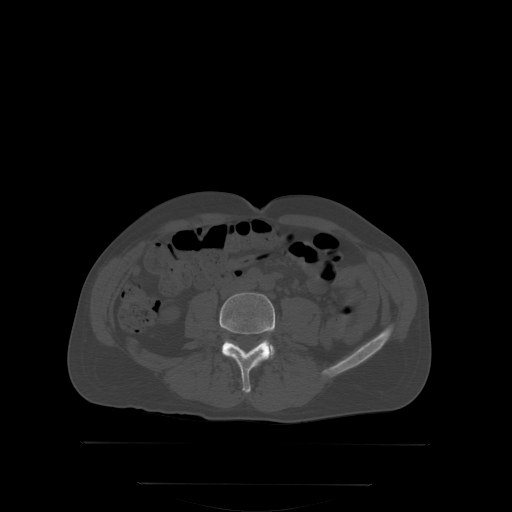
CT including the spine, one axial slice; slice 106 of 350 in the series (ordered by position); bone window (W 1800 / L 400 HU); 2.5 mm slice thickness; 512 × 512 image matrix, field of view 500 × 500 mm. Male patient, age 58 years. From the clinical record (not read from this slice): primary cancer: prostate.
Outlined on this slice (semi-automatic segmentation, software-assisted and operator-edited):
- L4 vertebra: box from (x=219, y=292) to (x=276, y=392) px
- L5 vertebra: (x=265, y=341)–(x=275, y=356)